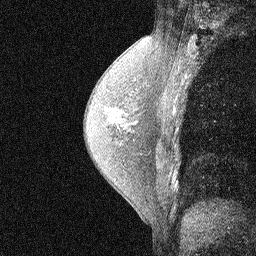
Breast MRI (dynamic contrast-enhanced), one sagittal slice; position 36 of 58 along the scan axis; dynamic contrast-enhanced study with each time point stored as its own series, time point 2 of 3 at this slice position (early post-contrast, ordered by acquisition time); 1.5 T; TE 4.5 ms, TR 11 ms; 2.07 mm slice thickness; 256 × 256 image matrix. Patient: female, 54 years. Case-level facts recorded for this patient, not image findings: setting: breast cancer imaged before/during neoadjuvant chemotherapy; receptor status: HR-positive, HER2-negative.
Structures marked on this image (semi-automatic segmentation, software-assisted and operator-edited):
- analysis volume of interest (the breast-tissue region the enhancement analysis was run in; not a lesion): bounding box <92,89,149,186> (left, top, right, bottom; pixels)
- tumour enhancement mask (voxels above the 90 % enhancement threshold inside the analysis volume of interest): <111,110,119,123>